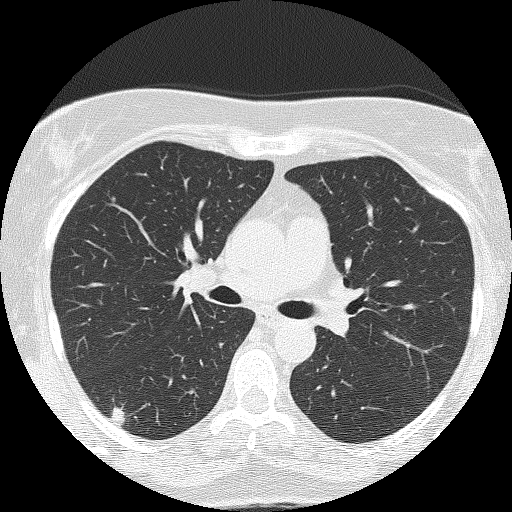
Low-dose screening chest CT, axial slice; second screening round (one year after baseline); lung window (W 1500 / L -600 HU); 2 mm slice thickness; lung (sharp) reconstruction kernel (FC51); slice 58 of 143 in the series; 512 × 512 image matrix. Female participant, aged 58 years at enrolment. Former smoker at enrolment.
Expert reader's lesion annotation, bounding box [x1, y1, x2, y2] px = [91, 394, 142, 431]. The screening reader recorded 2 non-calcified nodules or masses ≥4 mm on this exam (right upper lobe, right upper lobe); which of them this box marks is not recorded. Official screen result: positive, other. Lung cancer was diagnosed 264 days after this screen: adenocarcinoma, NOS, right lower lobe, well differentiated (G1), stage IB (AJCC 6th edition), 10 mm at pathology.